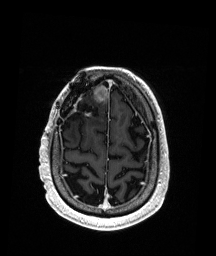
Brain MRI from a brain-tumour surgery series, one axial slice; position 43 of 192 along the scan axis; T1-weighted post-contrast; 1 mm slice thickness; 216 × 256 image matrix. From the clinical record (not read from this slice): histopathology: Astrocytoma; WHO grade: 3; IDH mutation: yes.
Outlined on this slice (outlined manually by an expert reader):
- previous resection cavity: bounding box <69,104,99,124> (left, top, right, bottom; pixels)
- tumour: <93,85,109,103>